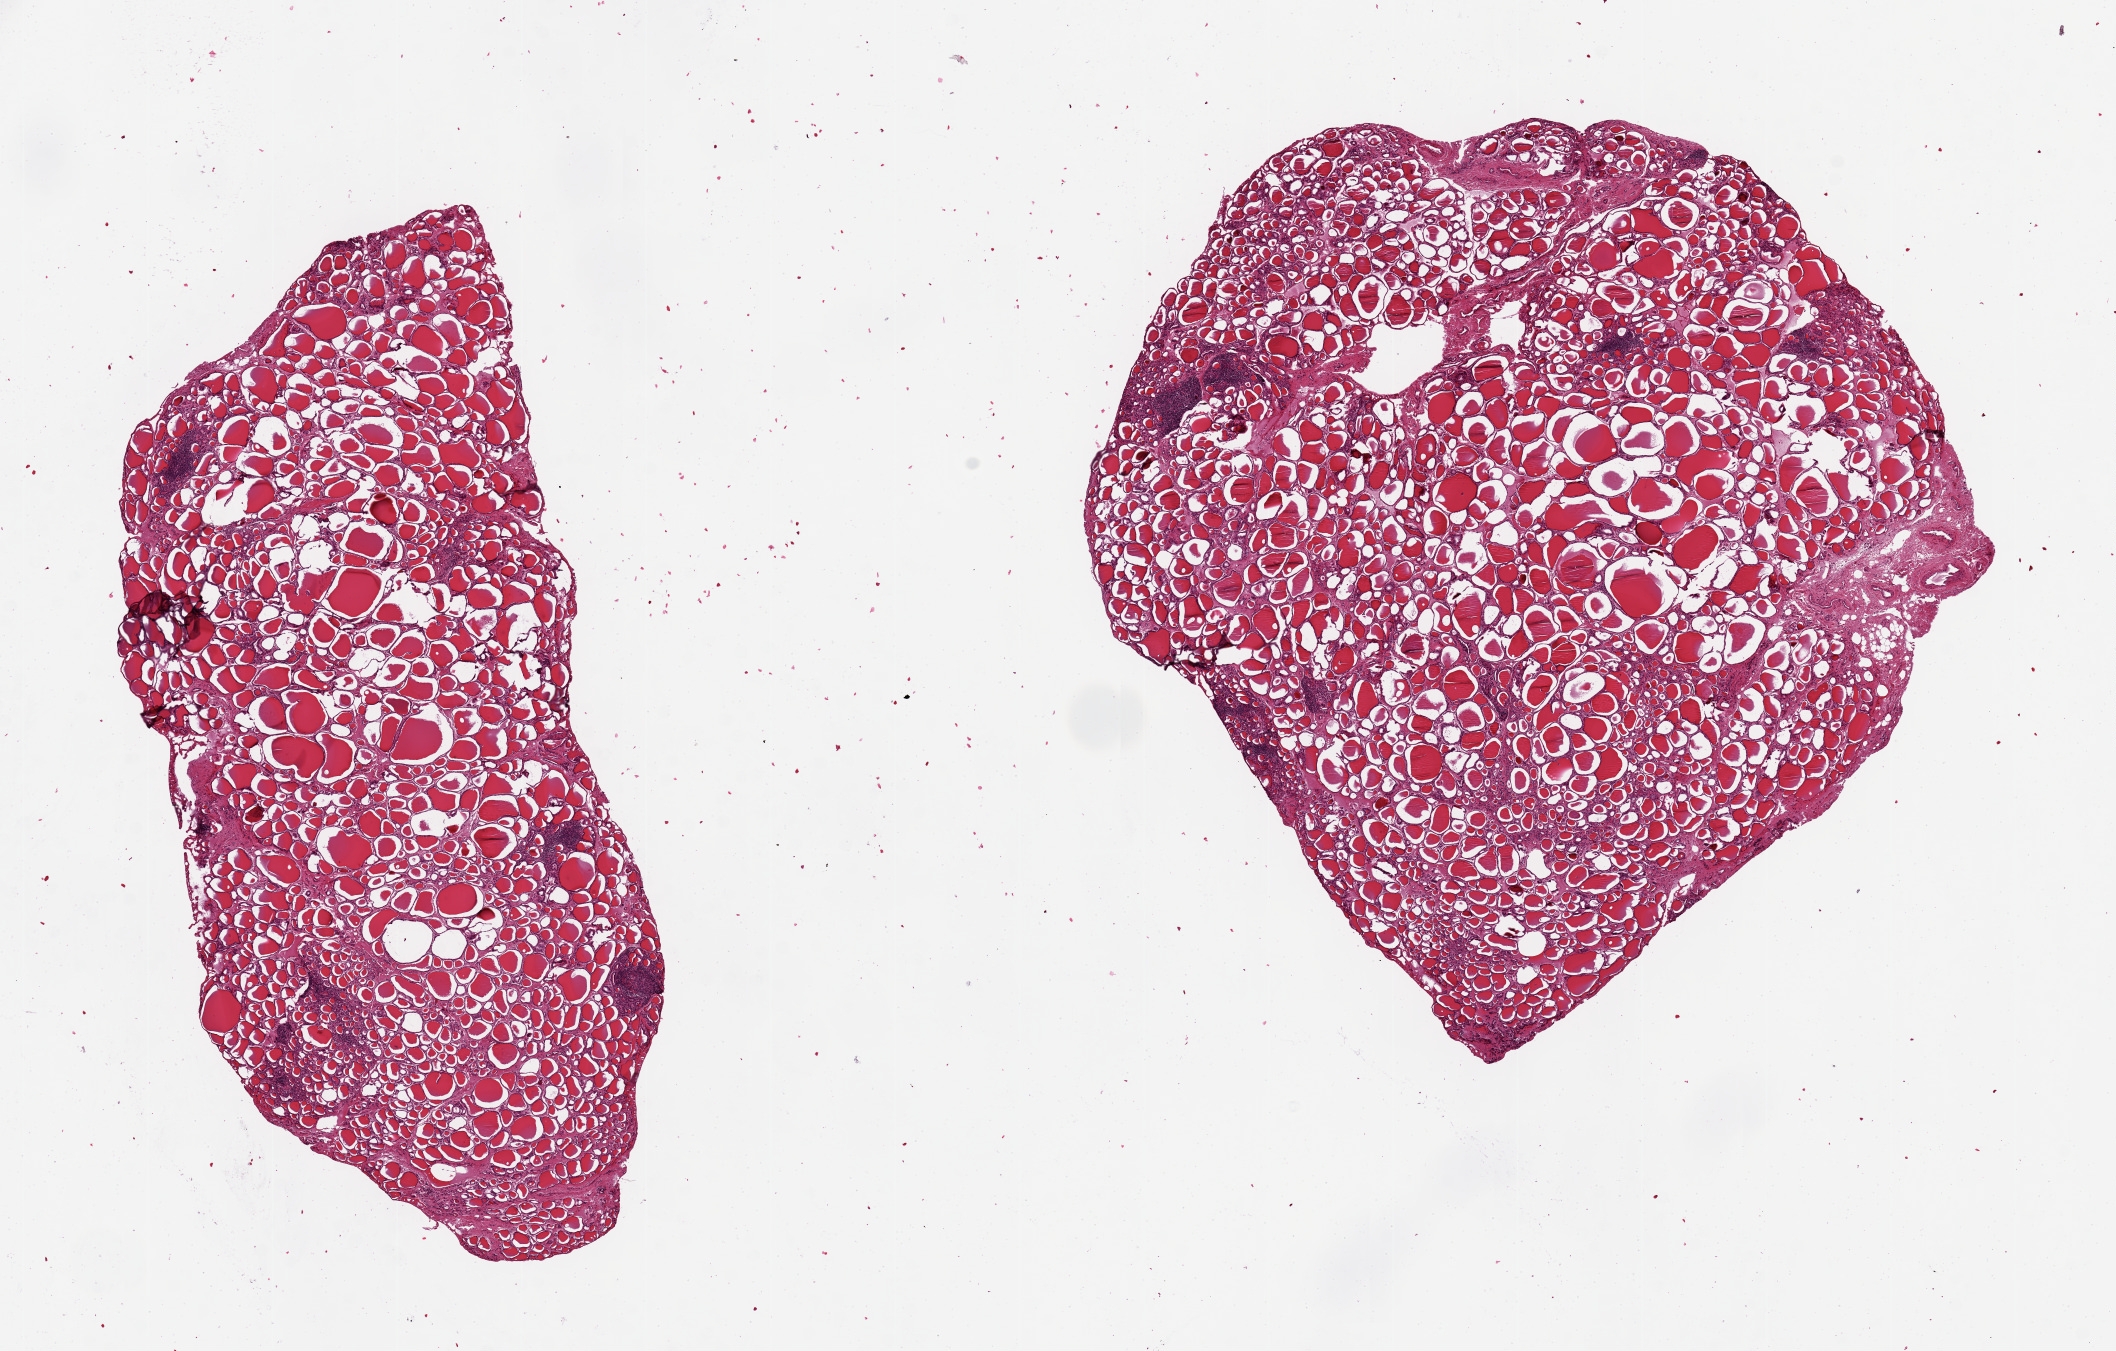
Digitized H&E-stained section — a low-resolution overview of the entire scanned area, about 16.7 x 10.7 mm (acquisition: 20x scan). PAXgene-fixed, paraffin-embedded tissue. Target tissue: thyroid. Tissue donor sample. Donor sex: male.
• reviewer comment on this tissue sample: 2 pieces, 8x4 & 7x6mm; mild lymphocytic infiltrate consistent with Hashimoto disease